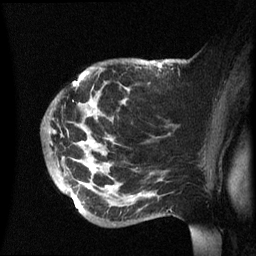
Breast MRI (dynamic contrast-enhanced), one sagittal slice; slice 42 of 60 in the series (ordered by position); dynamic contrast-enhanced series, image 2 of 3 at this slice position (ordered by acquisition); 1.5 T; TE 4.2 ms, TR 8.4 ms; 2.4 mm slice thickness; 256 × 256 image matrix, field of view 230 × 230 mm. Patient: female, 49 years.
Structures marked on this image (semi-automatically segmented with operator editing):
- analysis volume of interest (the breast-tissue region the enhancement analysis was run in; not a lesion): bounding box (x1, y1, x2, y2) in pixels: (43, 59, 174, 226)
- tumour enhancement mask (voxels above the 70 % enhancement threshold inside the analysis volume of interest): (73, 63, 161, 200)